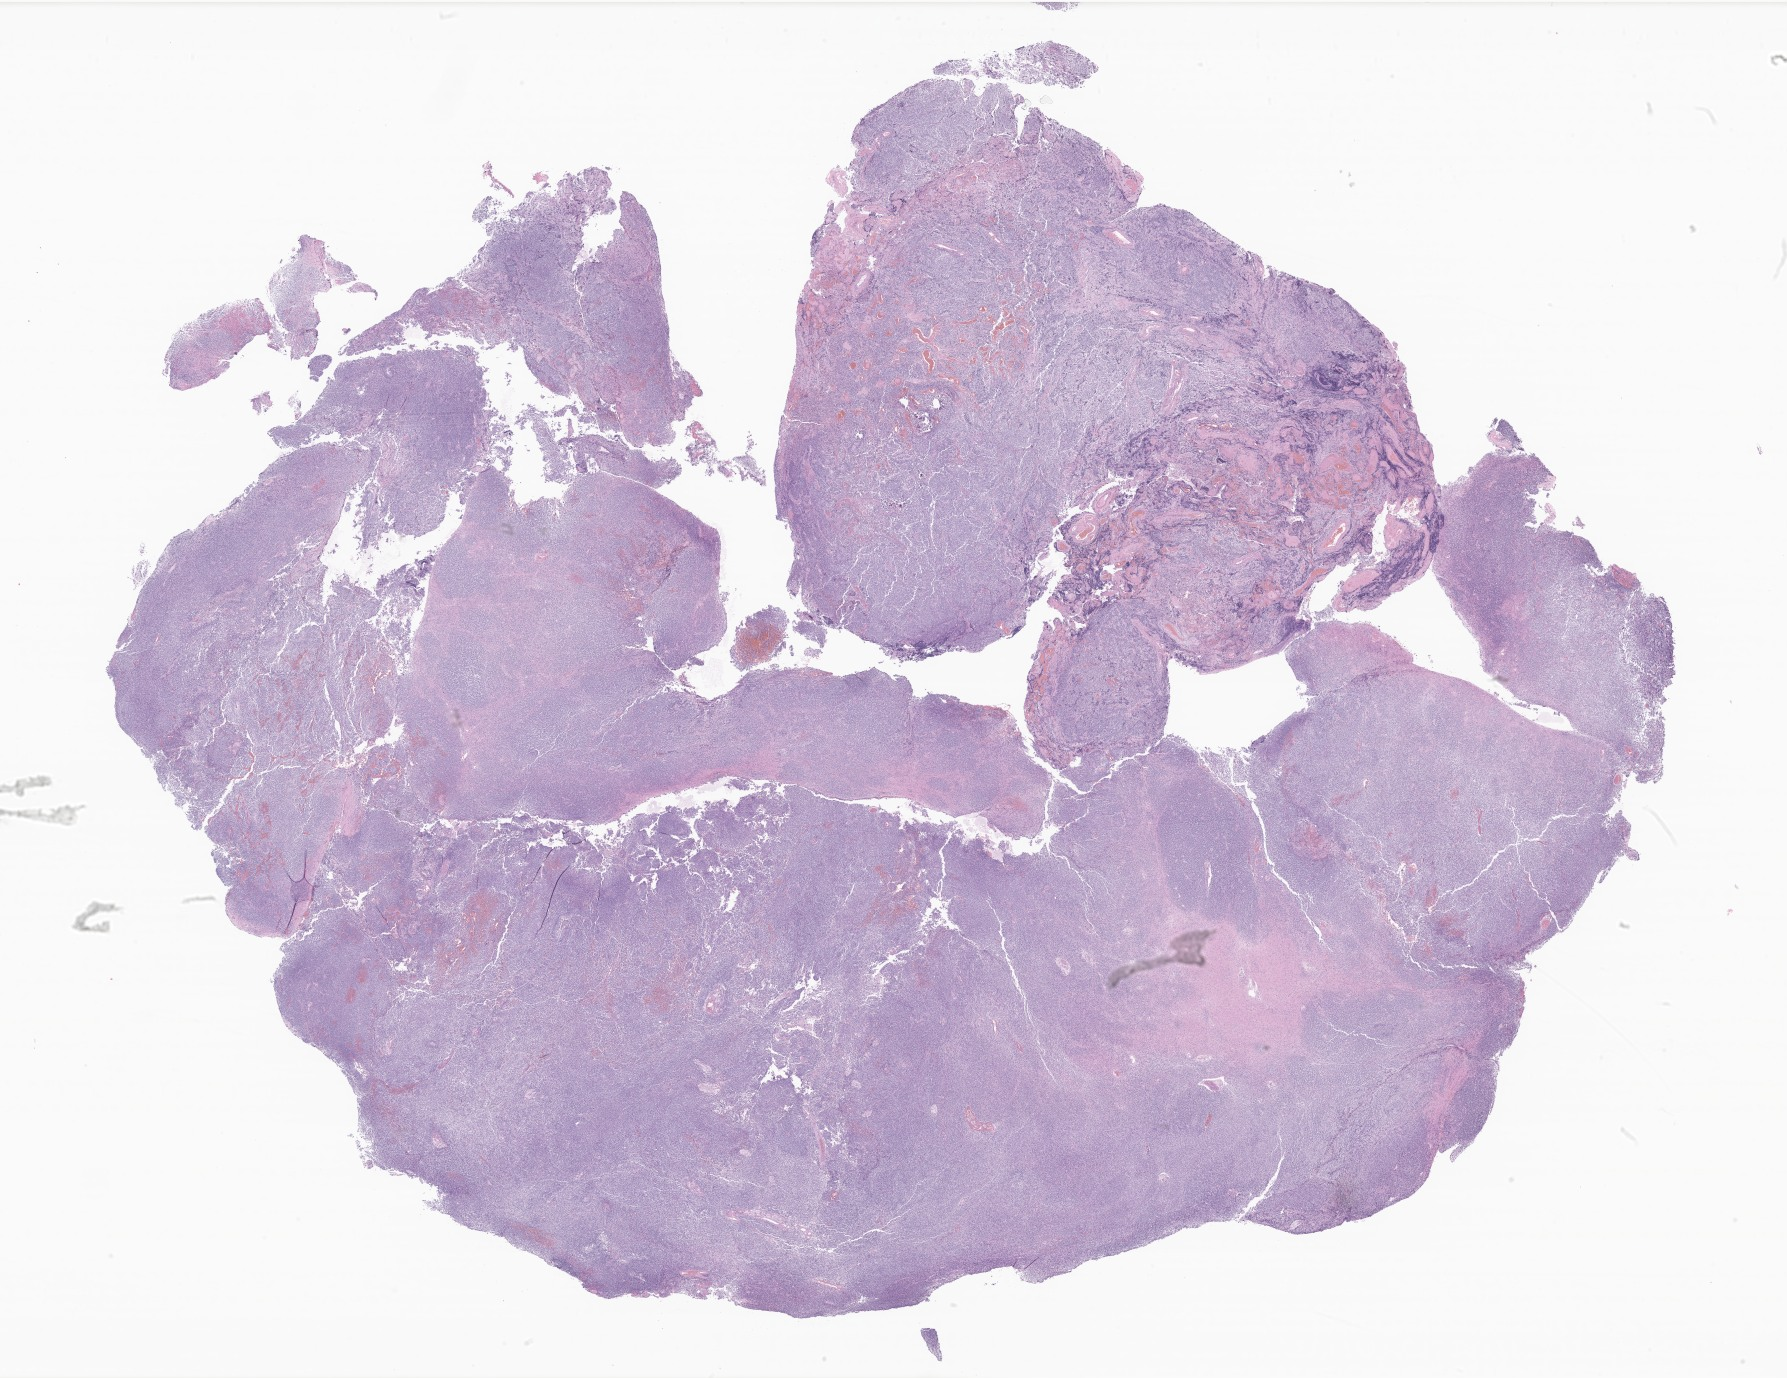
Hematoxylin and eosin (H&E) whole-slide image of tumor tissue from the brain, whole scanned area (about 30.1 x 23.2 mm) shown as a low-resolution overview, formalin-fixed, paraffin-embedded (FFPE) tissue. Male patient, age 123 months.
- diagnosis: Medulloblastoma, NOS